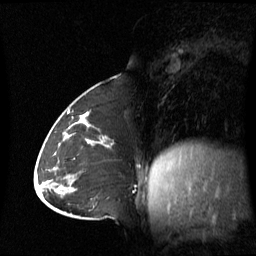
Breast MRI (dynamic contrast-enhanced), one sagittal slice. Position 27 of 60 along the scan axis. Dynamic contrast-enhanced series, image 2 of 3 at this slice position (ordered by acquisition). 1.5 T. TE 4.2 ms, TR 8.4 ms. 2.8 mm slice thickness. 256 × 256 image matrix. Patient: female, 43 years. Case-level facts recorded for this patient, not image findings: setting: breast cancer imaged before/during neoadjuvant chemotherapy; receptor status: triple-negative.
Outlined on this slice (semi-automatic segmentation, software-assisted and operator-edited):
- analysis volume of interest (the breast-tissue region the enhancement analysis was run in; not a lesion): box from (x=62, y=124) to (x=113, y=180) px
- tumour enhancement mask (voxels above the 70 % enhancement threshold inside the analysis volume of interest): (x=69, y=124)–(x=92, y=145)